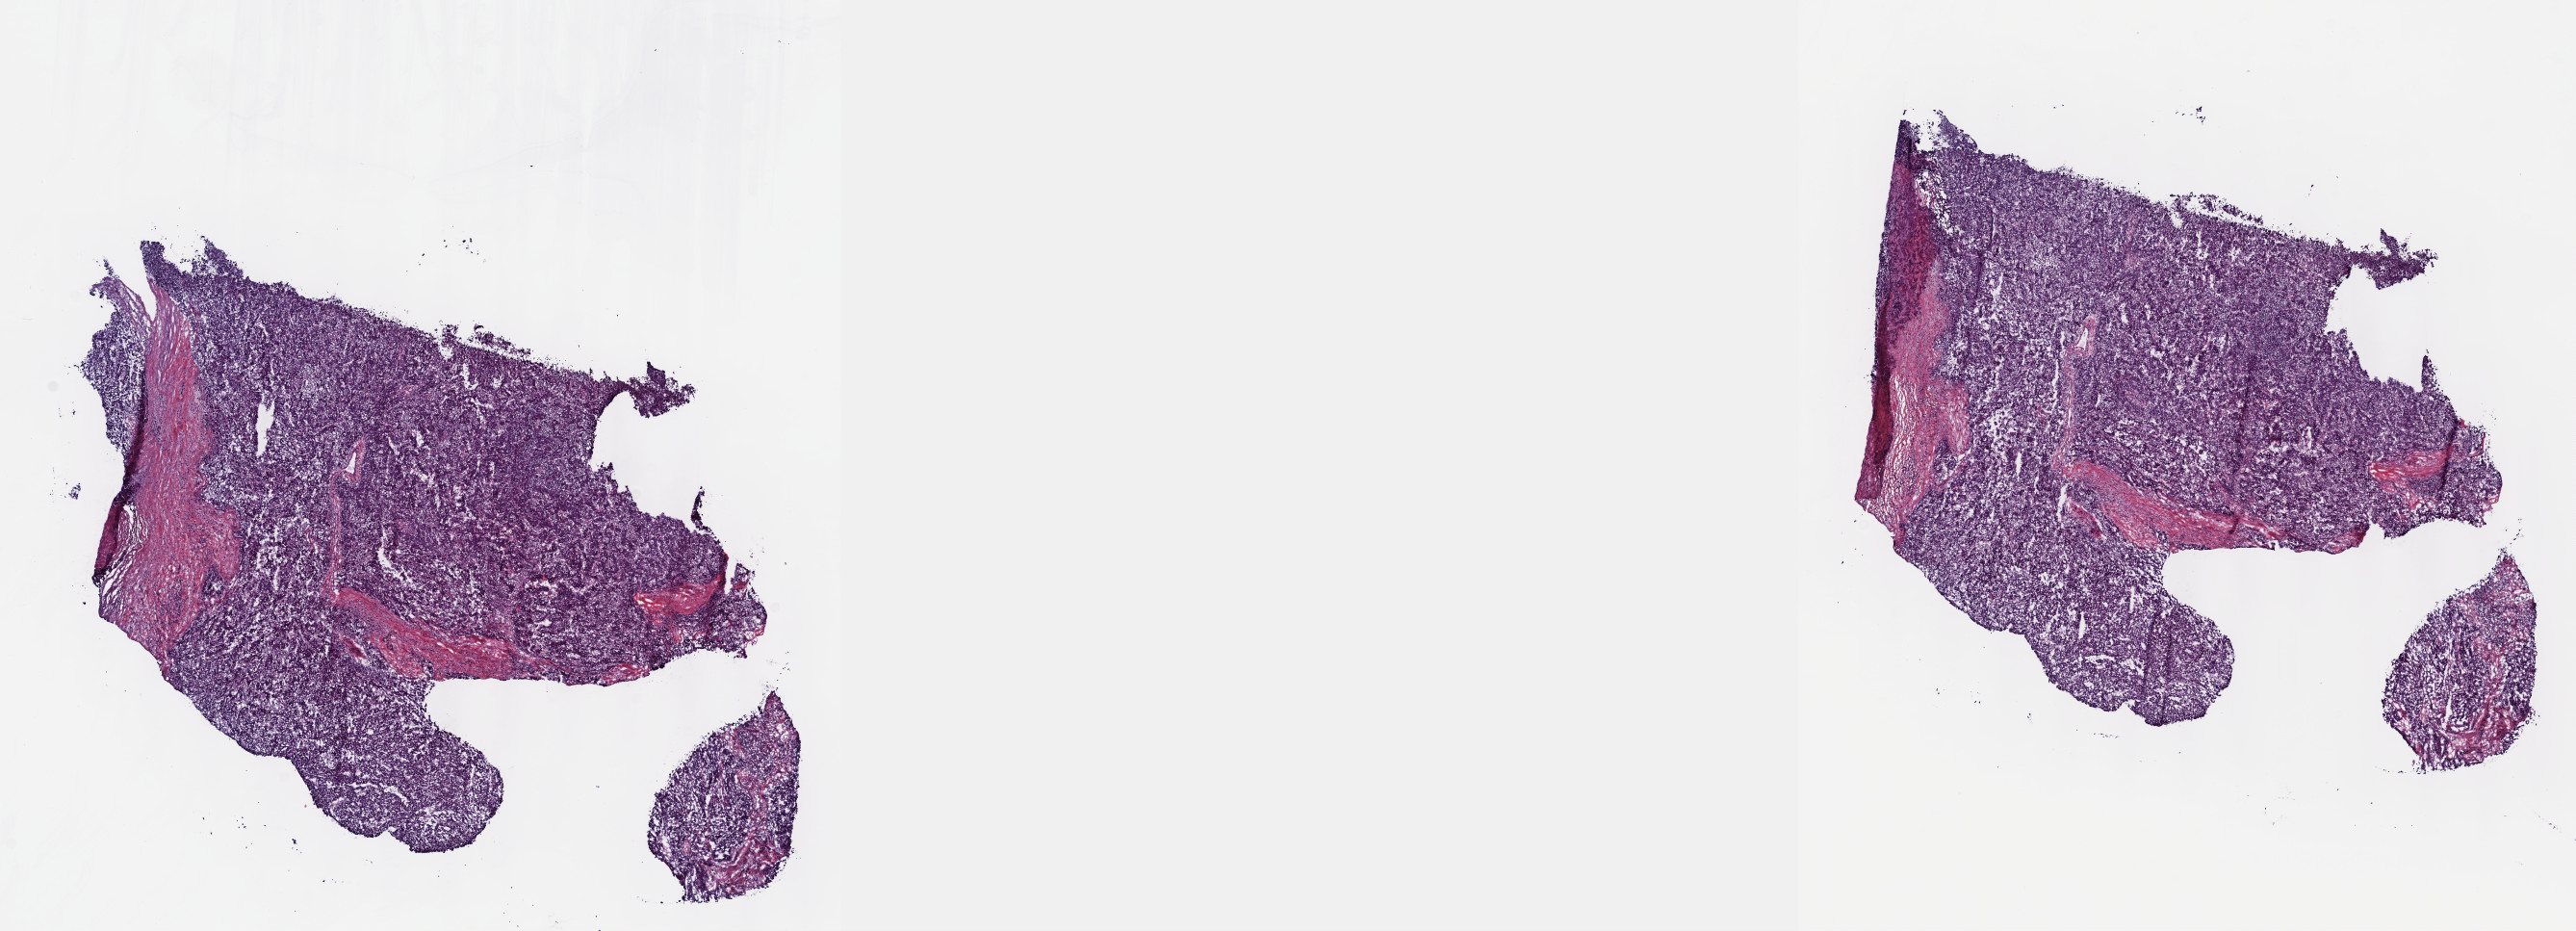
Hematoxylin and eosin (H&E) stained whole-slide image — whole scanned area (about 21.6 x 7.8 mm, from a 40x scan) shown as a low-resolution overview. Frozen section from the top of the tissue portion. Liver, primary tumour sample. Male patient. Histologic grade: G3 (poorly differentiated). Pathologist review of this section (percent, as recorded): tumour cells 50%, tumour nuclei 70%, normal cells 0%, stromal cells 30%, necrosis 20%. Infiltration values recorded for this section: lymphocyte infiltration 90%, monocyte infiltration 10%, neutrophil infiltration 0%.
TNM: T2 NX MX. AJCC pathologic stage: II (7th edition). Histologic diagnosis: Hepatocellular carcinoma, NOS.